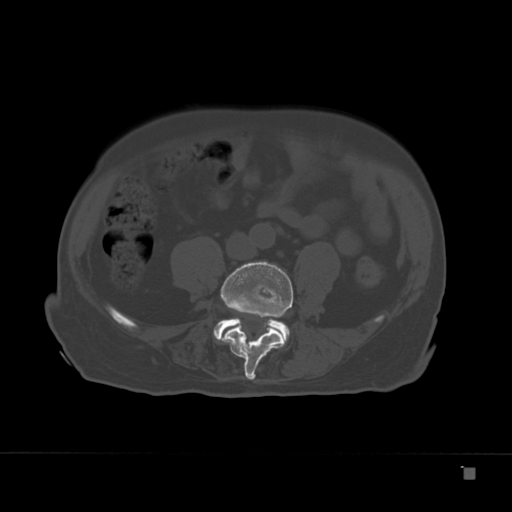
CT including the spine, one axial slice; position 38 of 332 along the scan axis; reconstruction kernel Br40s; 120 kVp; bone window (W 1800 / L 400 HU); 1.5 mm slice thickness; 512 × 512 image matrix, field of view 389 × 389 mm. Patient: male, 72 years. Case-level facts recorded for this patient, not image findings: primary cancer: skeletal.
Outlined on this slice (semi-automatically segmented with operator editing):
- L4 vertebra: bounding box [x1, y1, x2, y2] px = [223, 261, 293, 381]
- L5 vertebra: [214, 318, 290, 341]